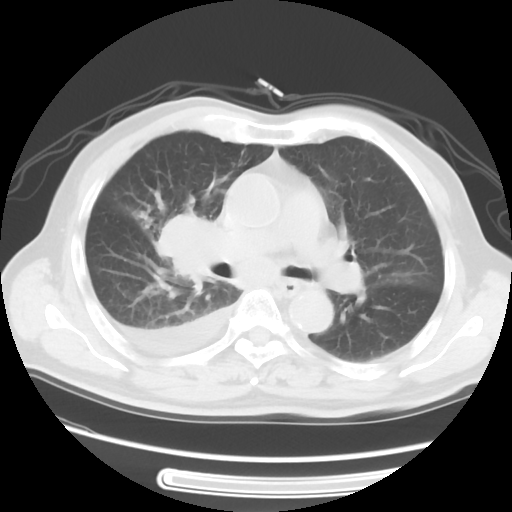
Chest CT, one axial slice. Slice 32 of 56 in the series (ordered by position). Reconstruction kernel STANDARD. Lung window (W 1500 / L -600 HU). 5 mm slice thickness. 512 × 512 image matrix. Male patient, age 77 years. Case-level facts recorded for this patient, not image findings: clinical TNM (as recorded): T3 N3 M1b; histopathological grade: G3.
Structures marked on this image (rectangle marked by the reading radiologist):
- lung tumour (recorded histology: small cell carcinoma): bounding box <142,209,225,292> (left, top, right, bottom; pixels)